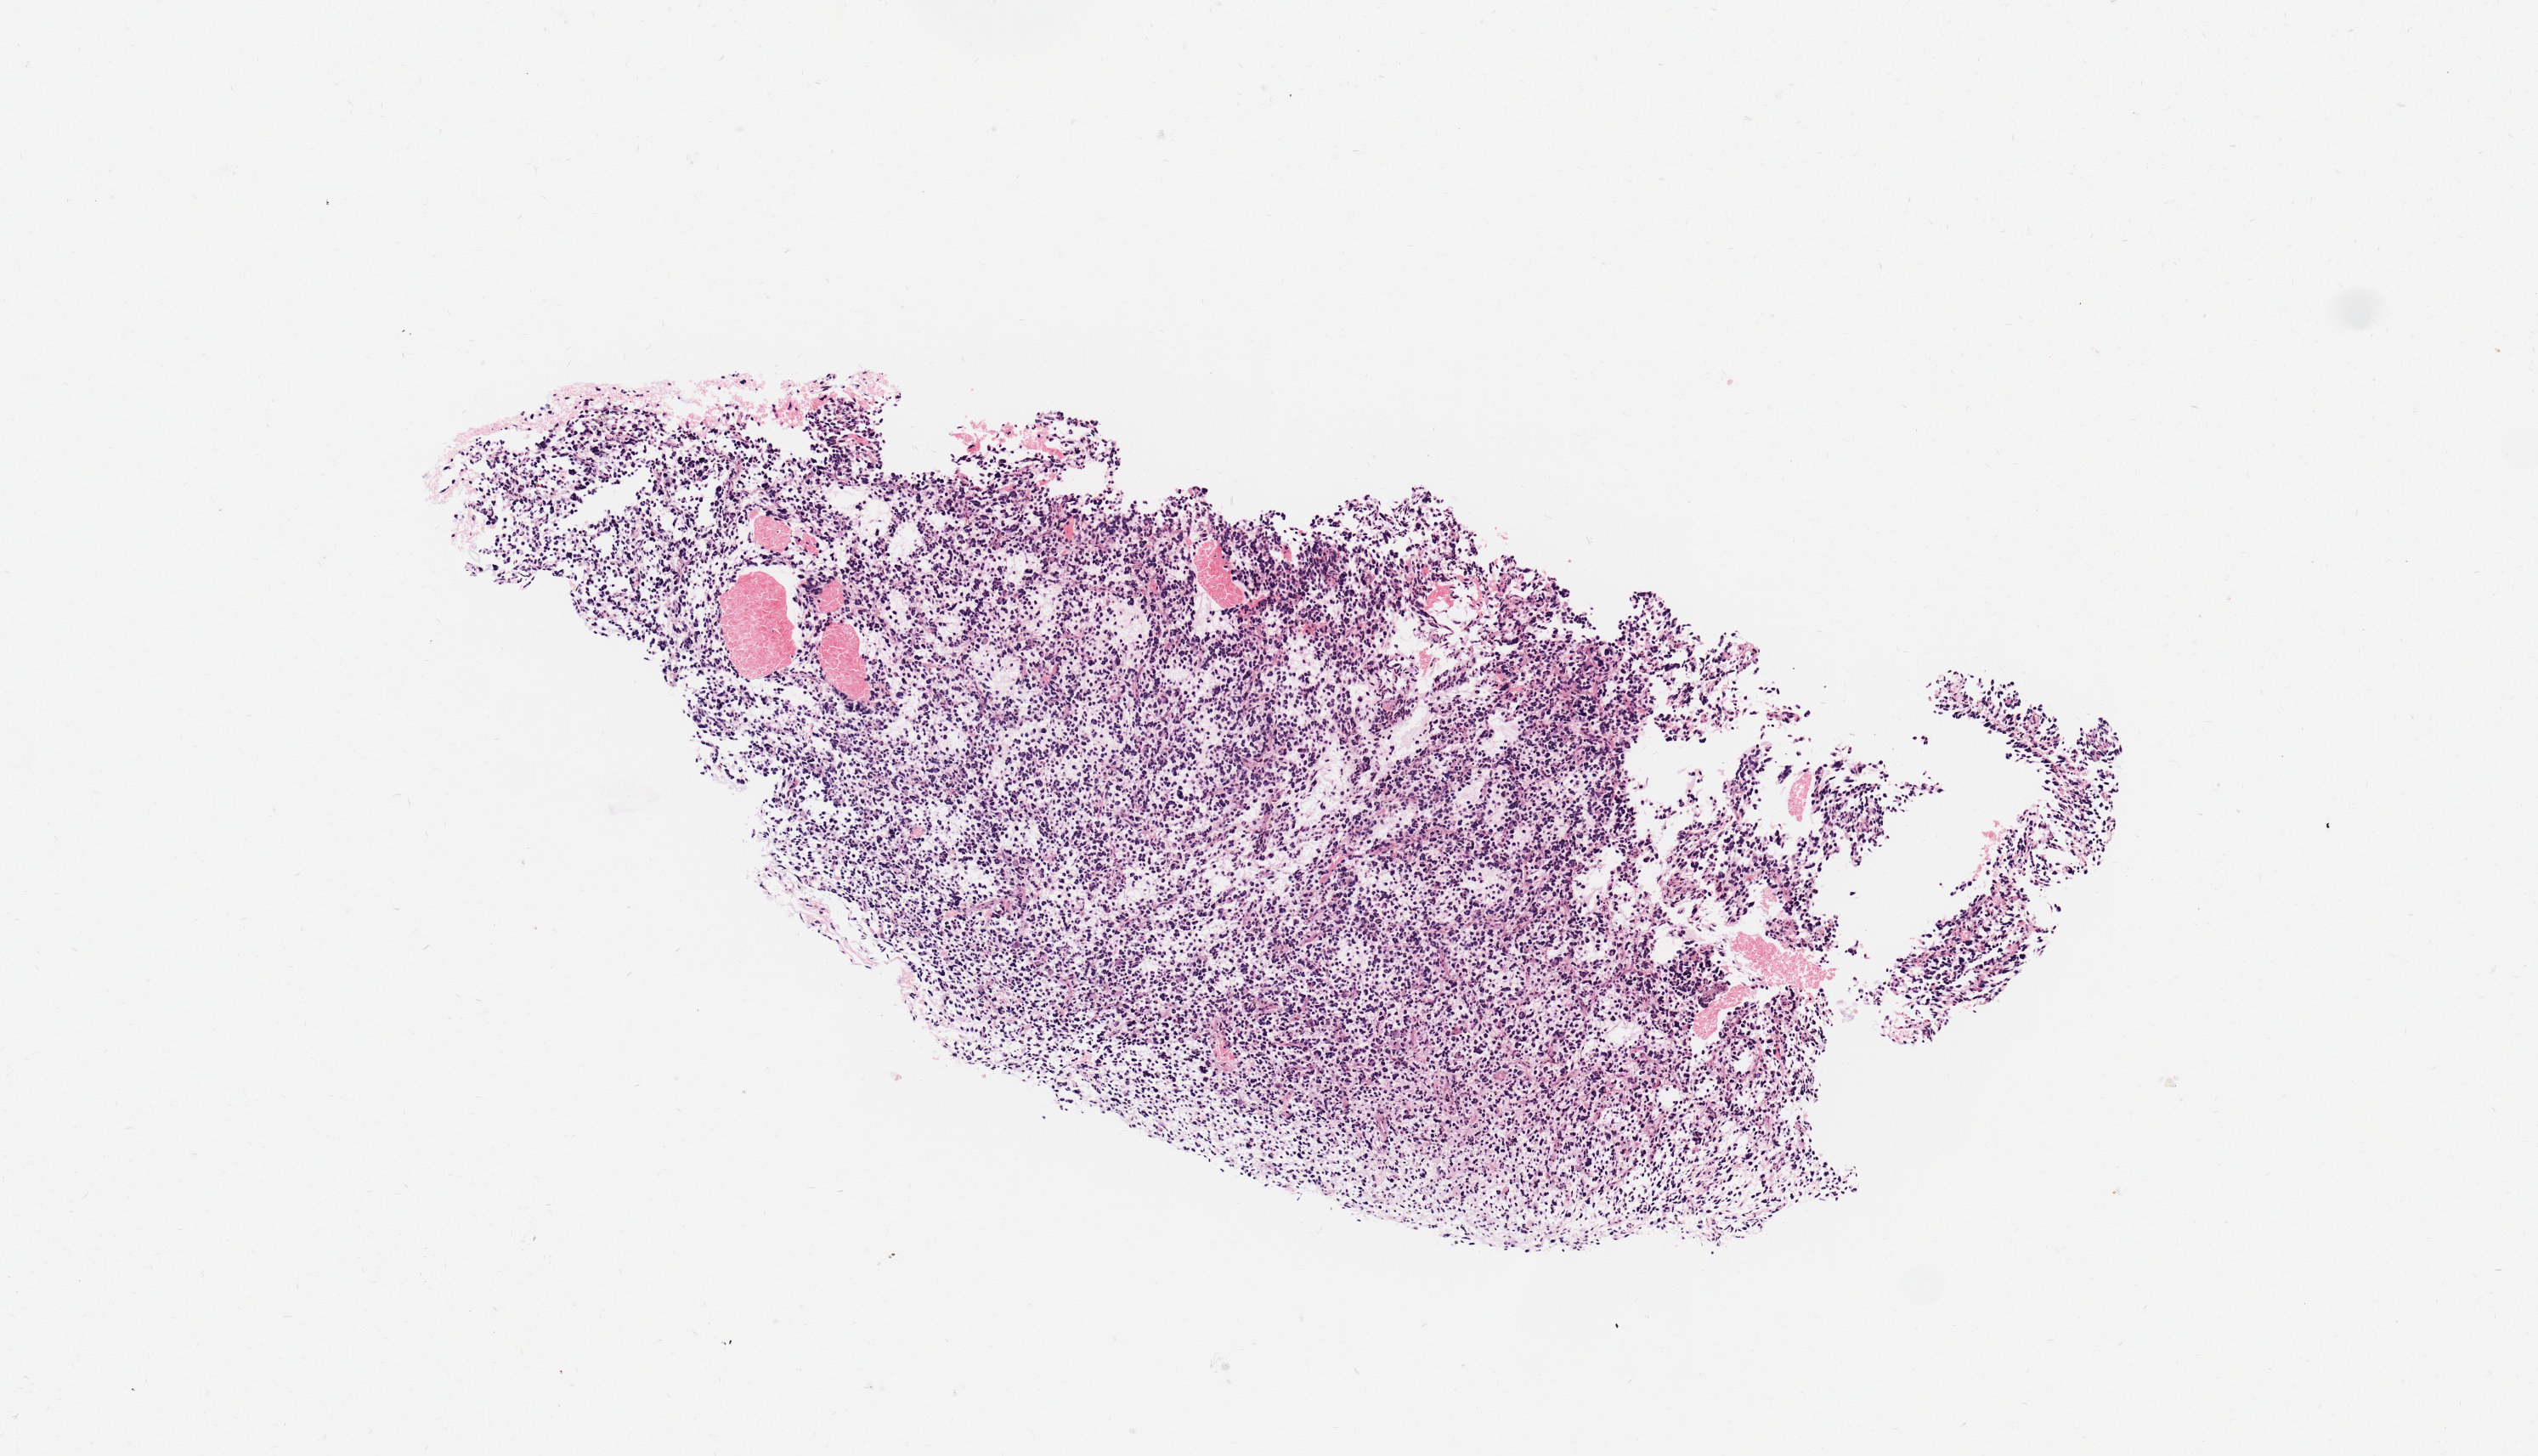
Whole-slide histology image, Hematoxylin and eosin (H&E) stained — low-resolution overview of the scanned area, about 5.9 x 3.4 mm (acquisition: 20x scan). Tumour tissue sample, sampled site: brain. Patient: female, age 65 years. Composition of this section per pathologist review: tumour nuclei 90%, necrosis 5%.
Diagnosis: Glioblastoma.